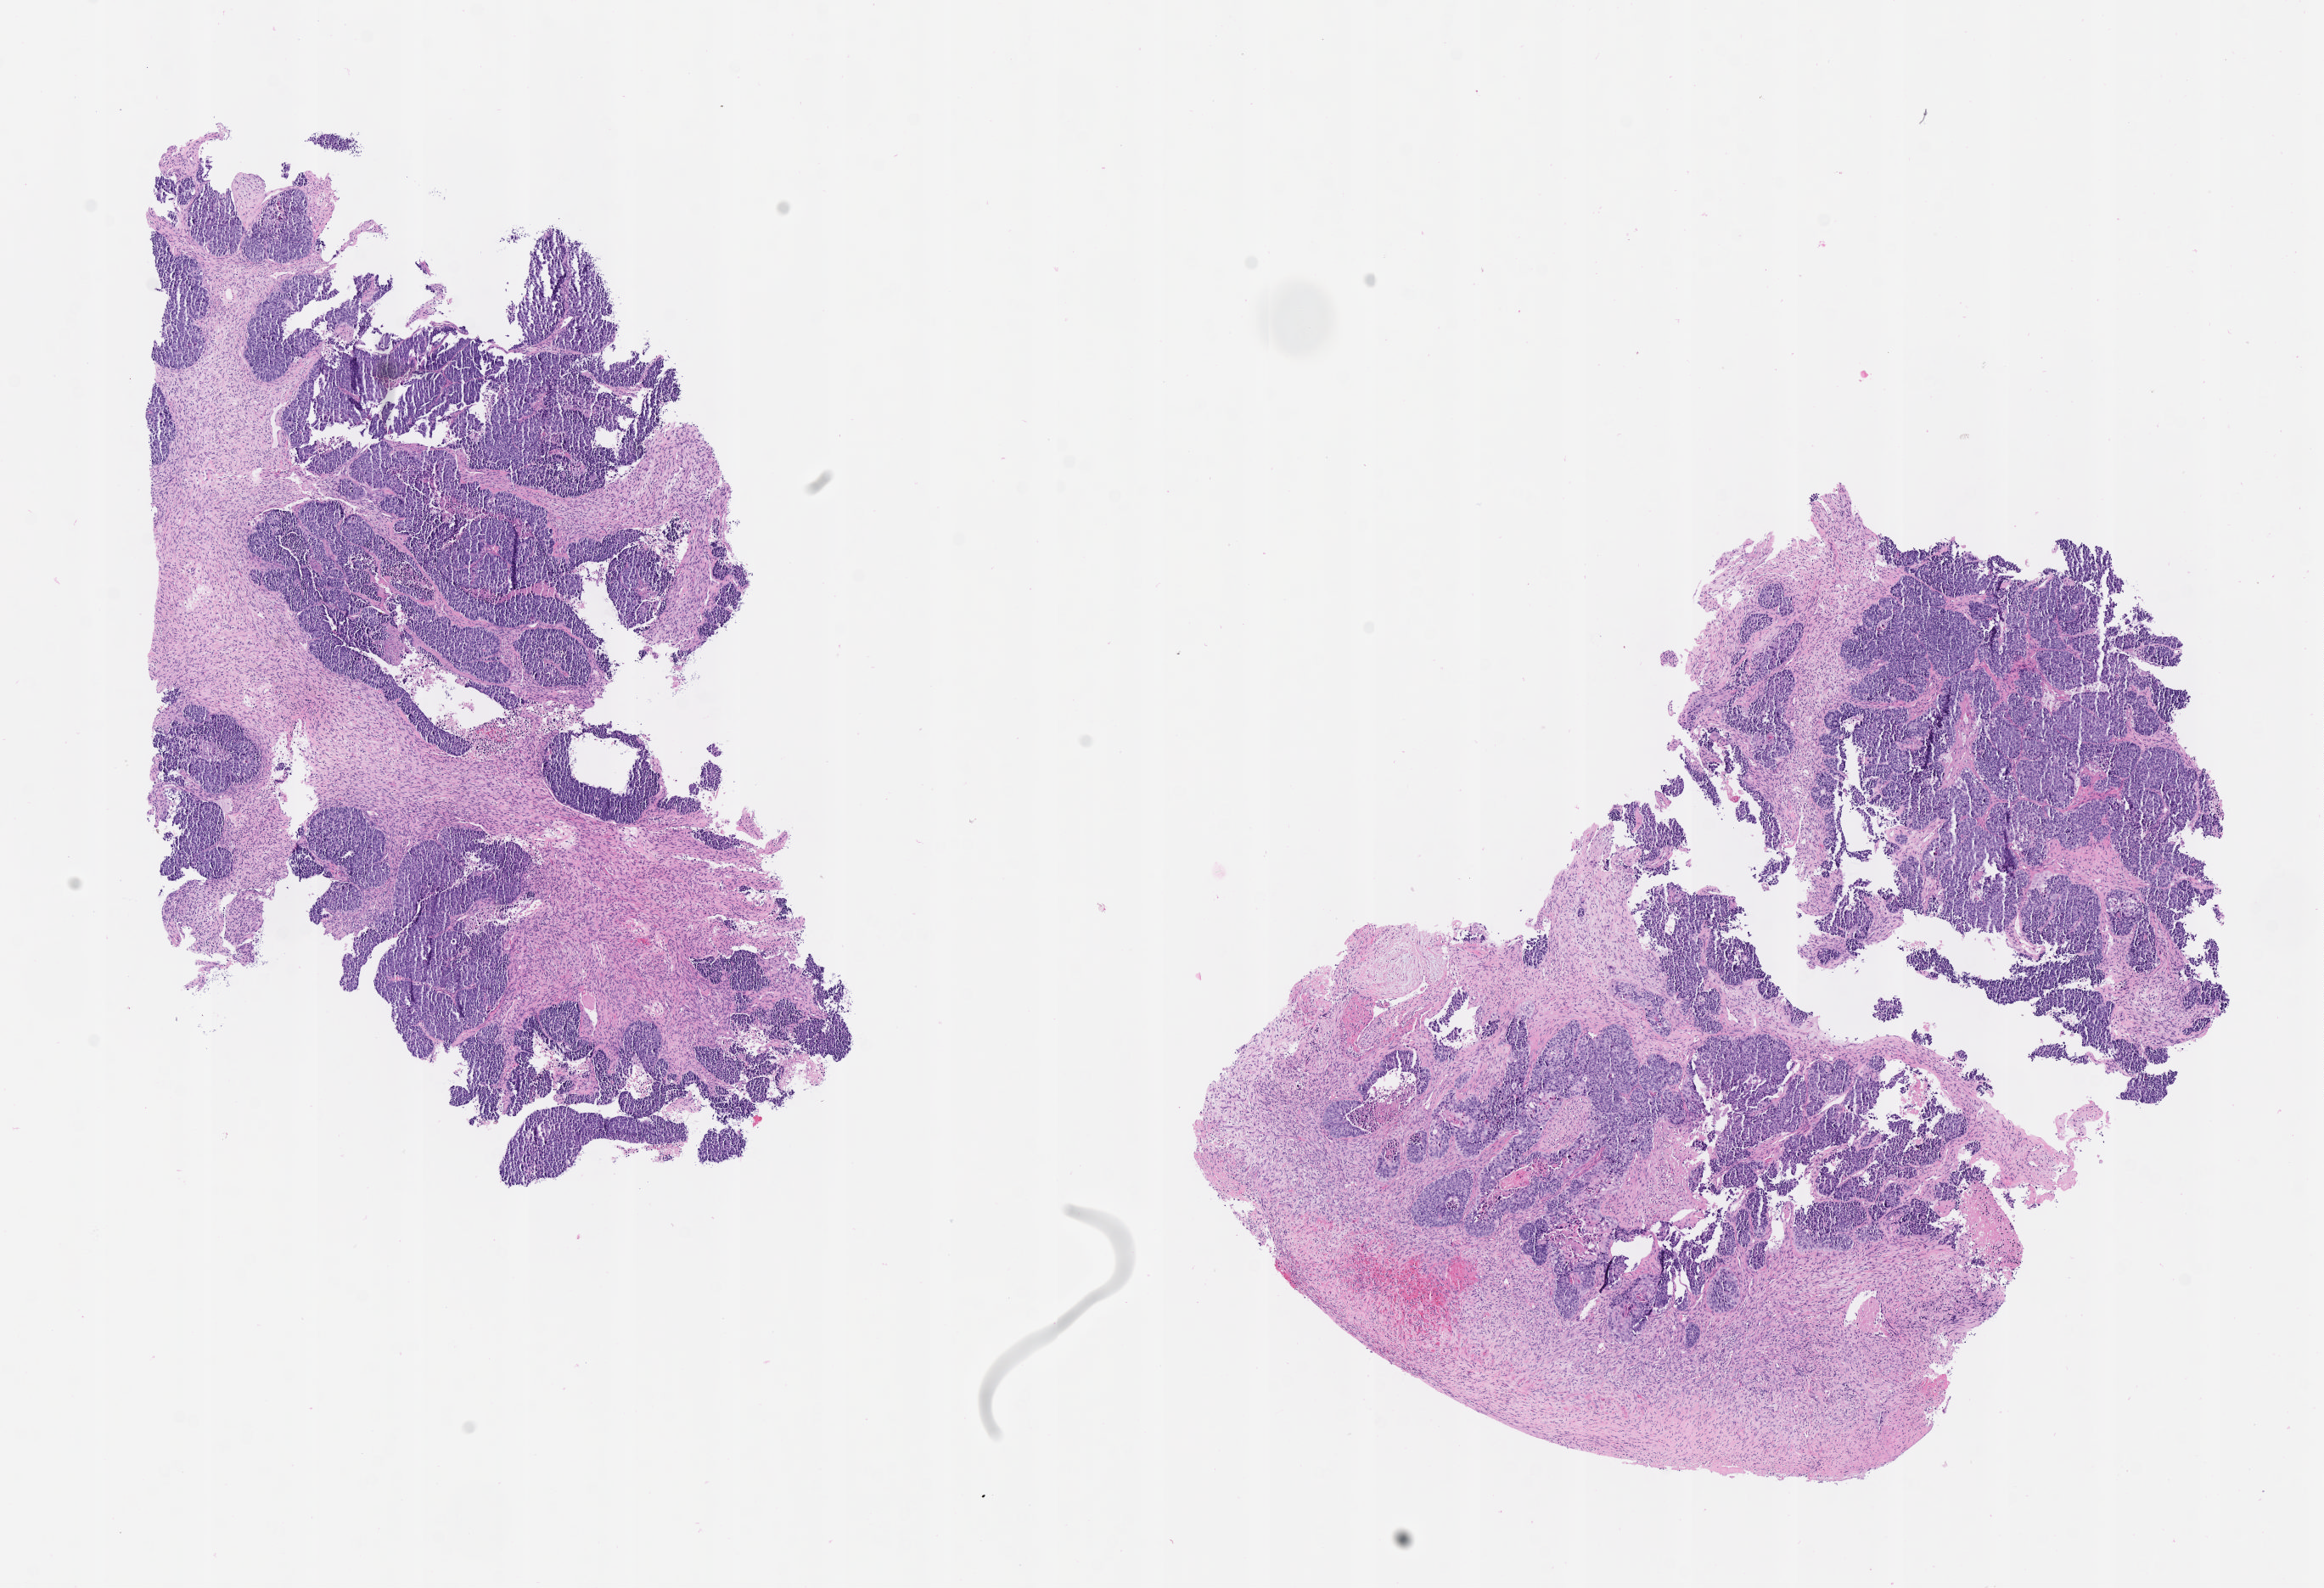
Whole-slide image, hematoxylin and eosin (H&E) stain — a low-resolution overview of the entire scanned area, about 11.1 x 7.6 mm, tumor tissue, site: cervix. Patient: female, age 38 years.
* diagnosis: Squamous cell carcinoma, large cell, nonkeratinizing, NOS